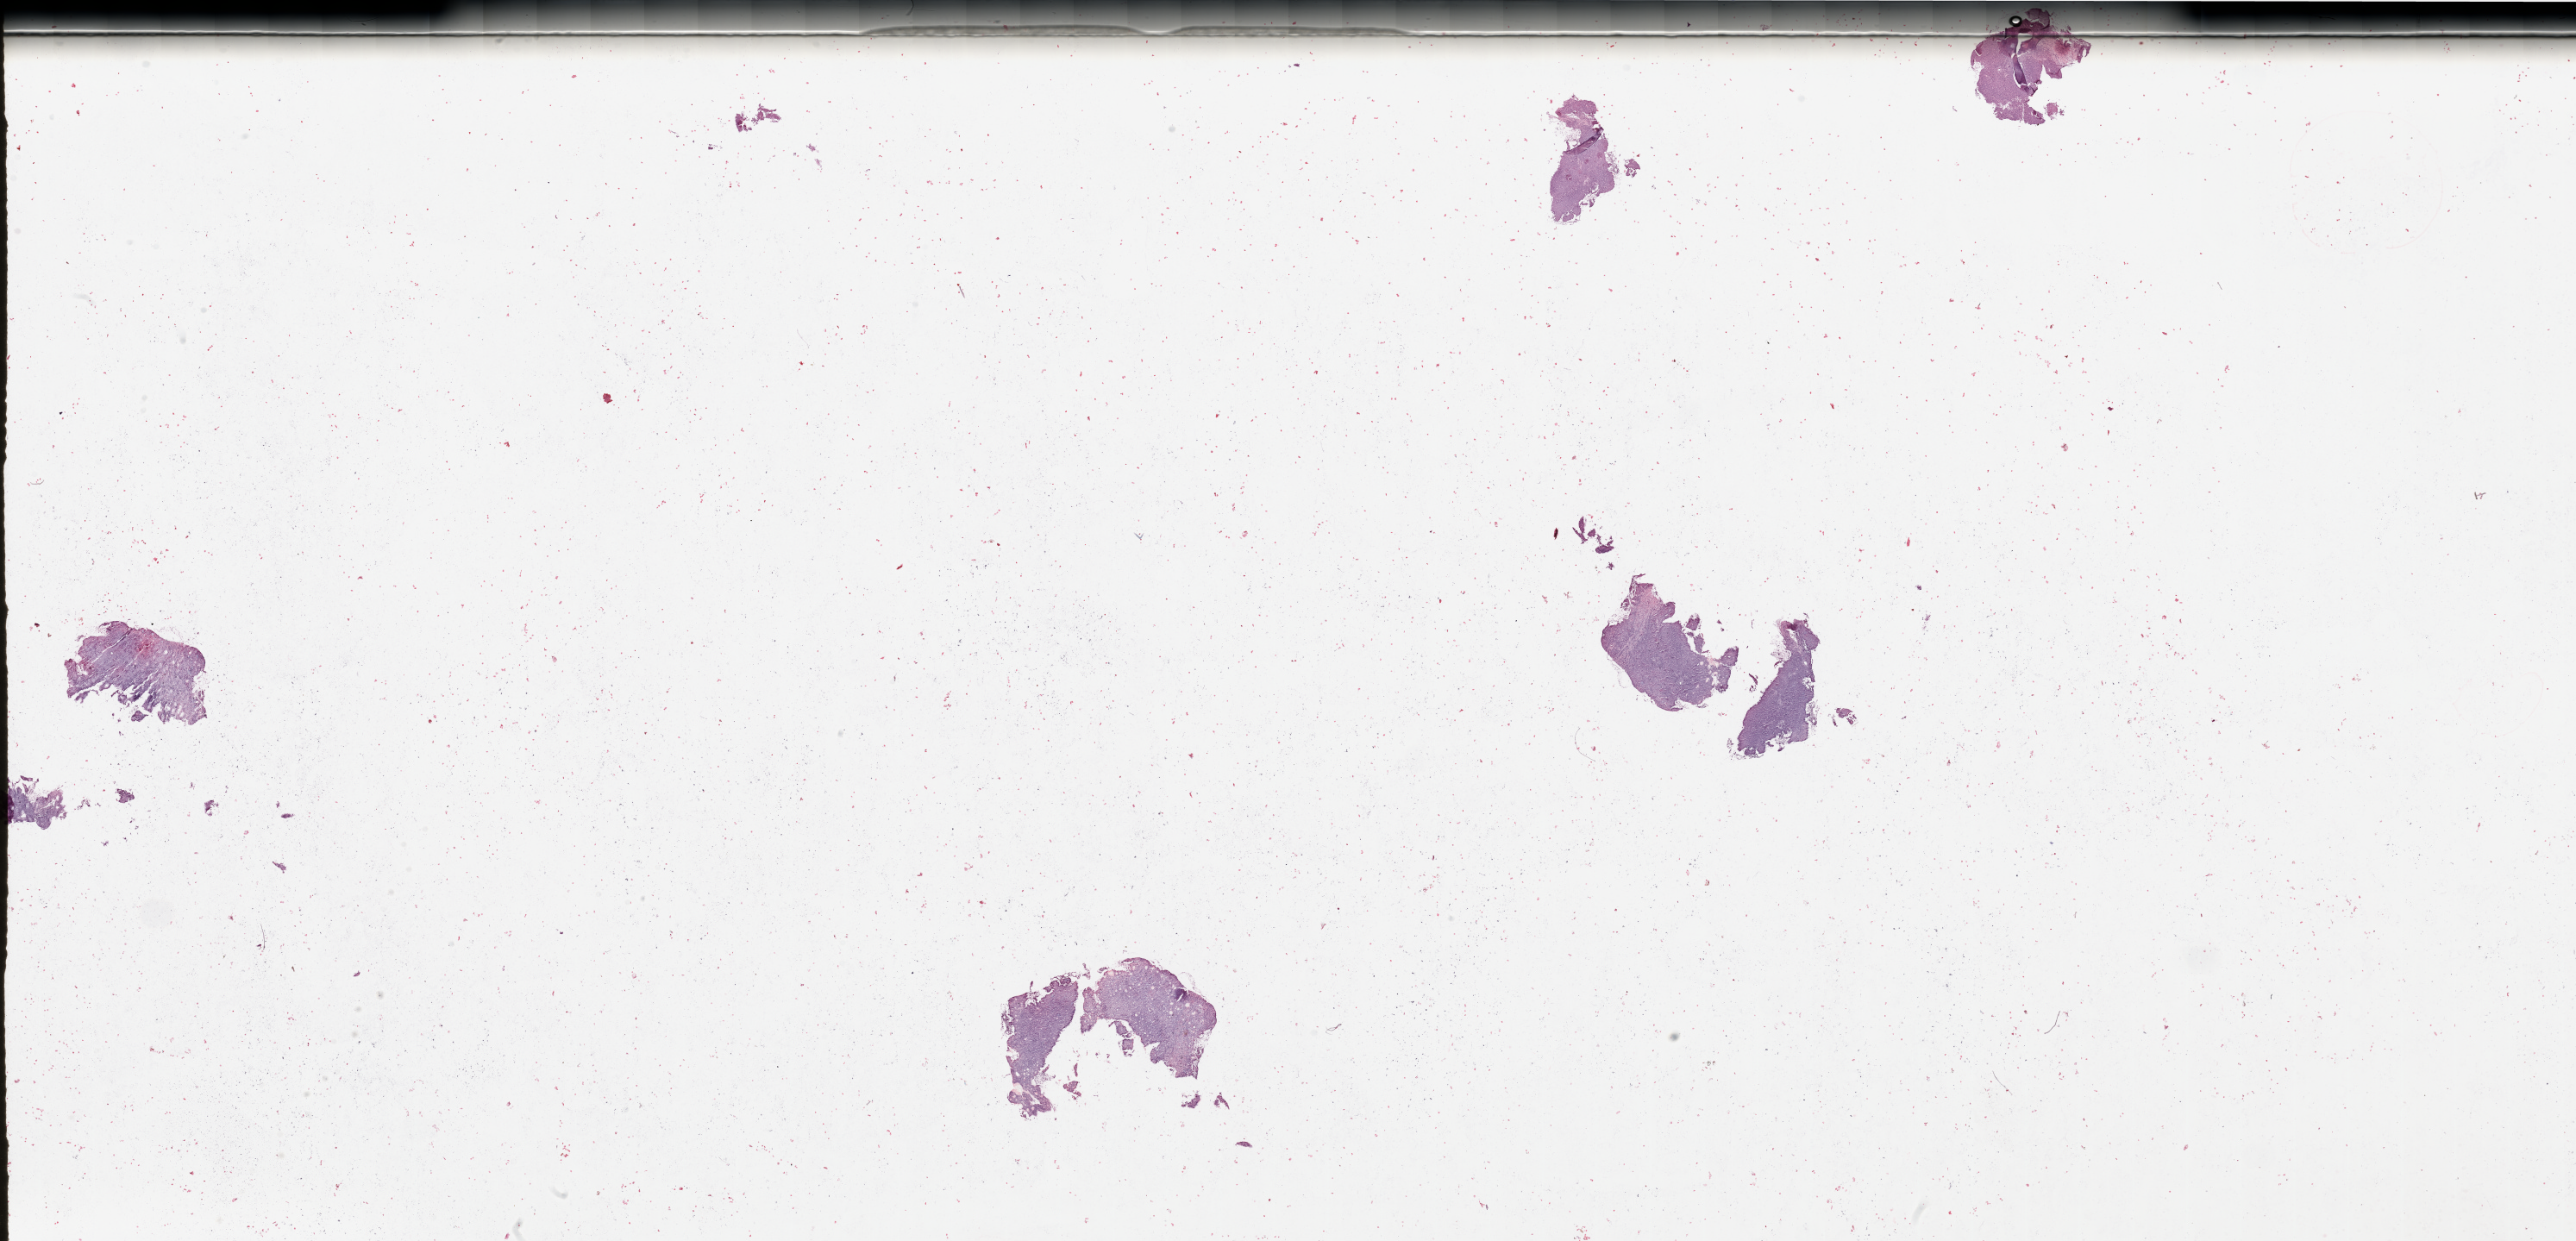
H&E-stained whole-slide image, low-resolution overview of the scanned area, about 47.3 x 22.8 mm (slide scanned at 20x); tumour tissue sample, sampled site: lymph node. Patient: female, age 55 years.
Patient diagnosis: Malignant melanoma, NOS.